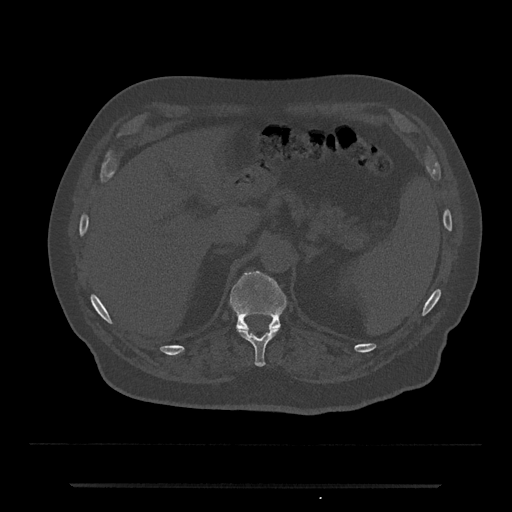
CT including the spine, one axial slice; position 622 of 797 along the scan axis; bone window (W 1800 / L 400 HU); 512 × 512 image matrix. Patient: male, 80 years. Case-level facts recorded for this patient, not image findings: primary cancer: prostate.
Outlined on this slice (semi-automatically segmented with operator editing):
- T11 vertebra: bounding box (x1, y1, x2, y2) in pixels: (238, 329, 278, 367)
- T12 vertebra: (229, 270, 287, 342)